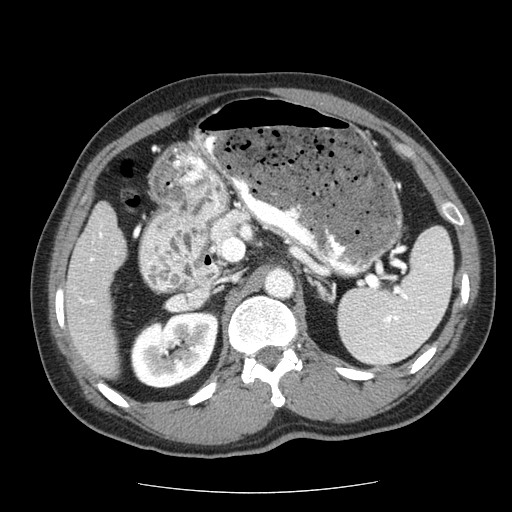
Contrast-enhanced abdominal CT (liver protocol), one axial slice. Slice 23 of 85 in the series (ordered by position). Reconstruction kernel STANDARD. Soft-tissue window (W 400 / L 40 HU). 2.5 mm slice thickness. 512 × 512 image matrix. From the clinical record (not read from this slice): diagnosis: hepatocellular carcinoma (patient treated with transarterial chemoembolisation; whether this scan precedes or follows treatment is not stated here); TNM stage (as recorded): Stage-IIIA; Child-Pugh class: A; tumour nodularity: multinodular.
Annotated regions visible in this slice (semi-automatically segmented with operator editing):
- liver parenchyma outside the tumour (the mass and vessels are separate outlines, so this box may not span the whole liver): box from (x=64, y=202) to (x=126, y=378) px
- liver vessels: (x=79, y=233)–(x=103, y=303)